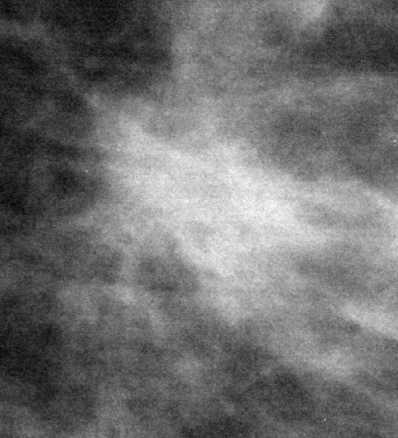
Cropped region of a digitized screen-film mammogram centred on a radiologist-marked abnormality, left breast, MLO view, BI-RADS breast density category 2 (scale 1–4).
Finding: mass, shape irregular, margins spiculated; BI-RADS assessment category 5; subtlety rating 5 on a 1 (subtle) to 5 (obvious) scale; pathology (as recorded): malignant.